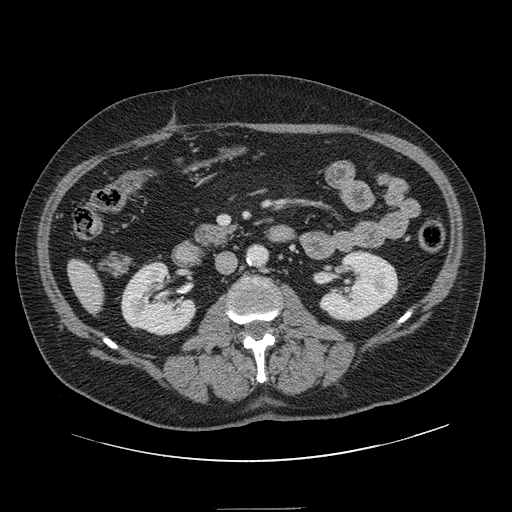
Contrast-enhanced abdominal CT, one axial slice. Position 37 of 154 along the scan axis. 120 kVp. Intravenous contrast given. Soft-tissue window (W 400 / L 40 HU). 2.5 mm slice thickness. 512 × 512 image matrix, field of view 451 × 451 mm. Male patient, age 61 years. From the clinical record (not read from this slice): diagnosis: colorectal cancer liver metastases, imaged before liver resection; multiple liver metastases: yes; largest metastasis: 2.6 cm; disease in both lobes: yes.
Structures marked on this image (expert manual segmentation):
- liver: bounding box <69,262,105,312> (left, top, right, bottom; pixels)
- planned liver remnant (the part of the liver to remain after resection): <69,261,104,313>